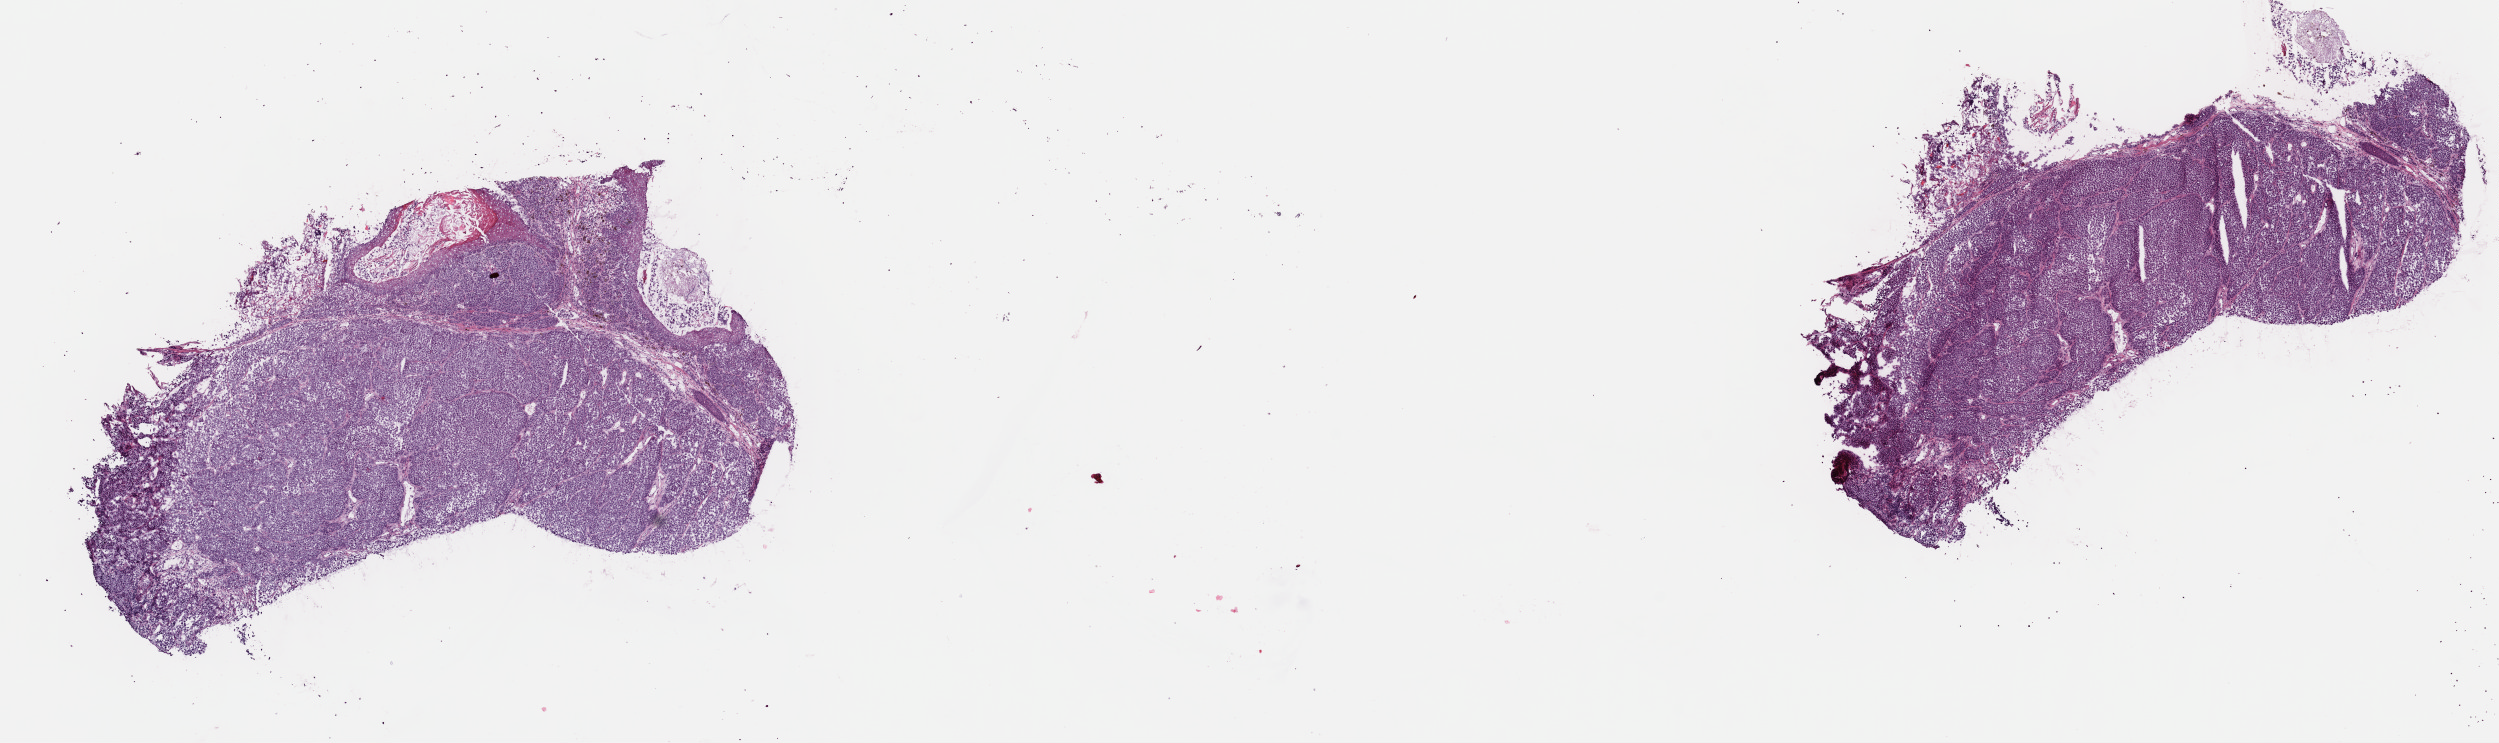
Whole-slide histology image, Hematoxylin and eosin (H&E) stained, a low-resolution overview of the entire scanned area, about 19.7 x 5.9 mm (from a 40x scan); frozen section from the top of the tissue portion; sample: primary tumour, skin. Male patient; age at initial diagnosis 48 years. Slide review estimates, as recorded: tumour cells 80%, tumour nuclei 80%, normal cells 10%, stromal cells 10%, necrosis 0%. Inflammatory infiltration, as recorded: lymphocyte infiltration 3%, monocyte infiltration 0%, neutrophil infiltration 0%.
Histologic diagnosis: Malignant melanoma, NOS.